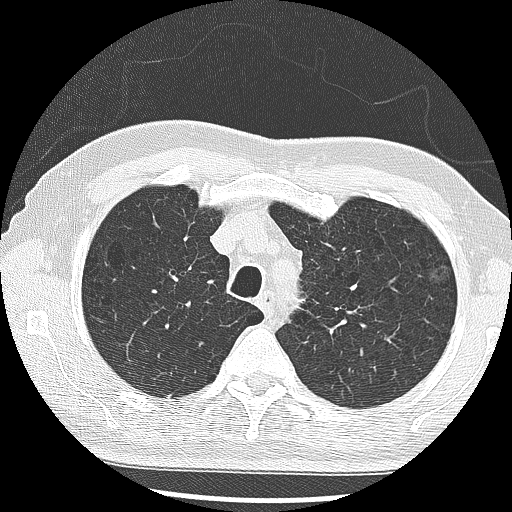
Low-dose screening chest CT, one axial slice. Position 222 of 285 along the scan axis. 120 kVp. Lung window (W 1500 / L -600 HU). 2.5 mm slice thickness. 512 × 512 image matrix, field of view 340 × 340 mm.
Structures marked on this image (manually delineated by an expert):
- lesion 1 (tumor, upper lobe of left lung): bounding box (x1, y1, x2, y2) in pixels: (430, 266, 450, 282)